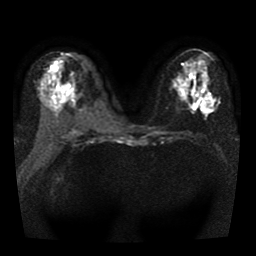
Breast MRI, one axial slice; slice 18 of 41 in the series (ordered by position); diffusion-weighted series; image 2 of 4 stored at this slice position (different b-values; order by instance number); 1.5 T; 5 mm slice thickness; 256 × 256 image matrix, field of view 330 × 330 mm. Female patient.
Structures marked on this image (manually delineated by an expert):
- tumour on diffusion-weighted imaging: bounding box [x1, y1, x2, y2] px = [204, 96, 214, 108]